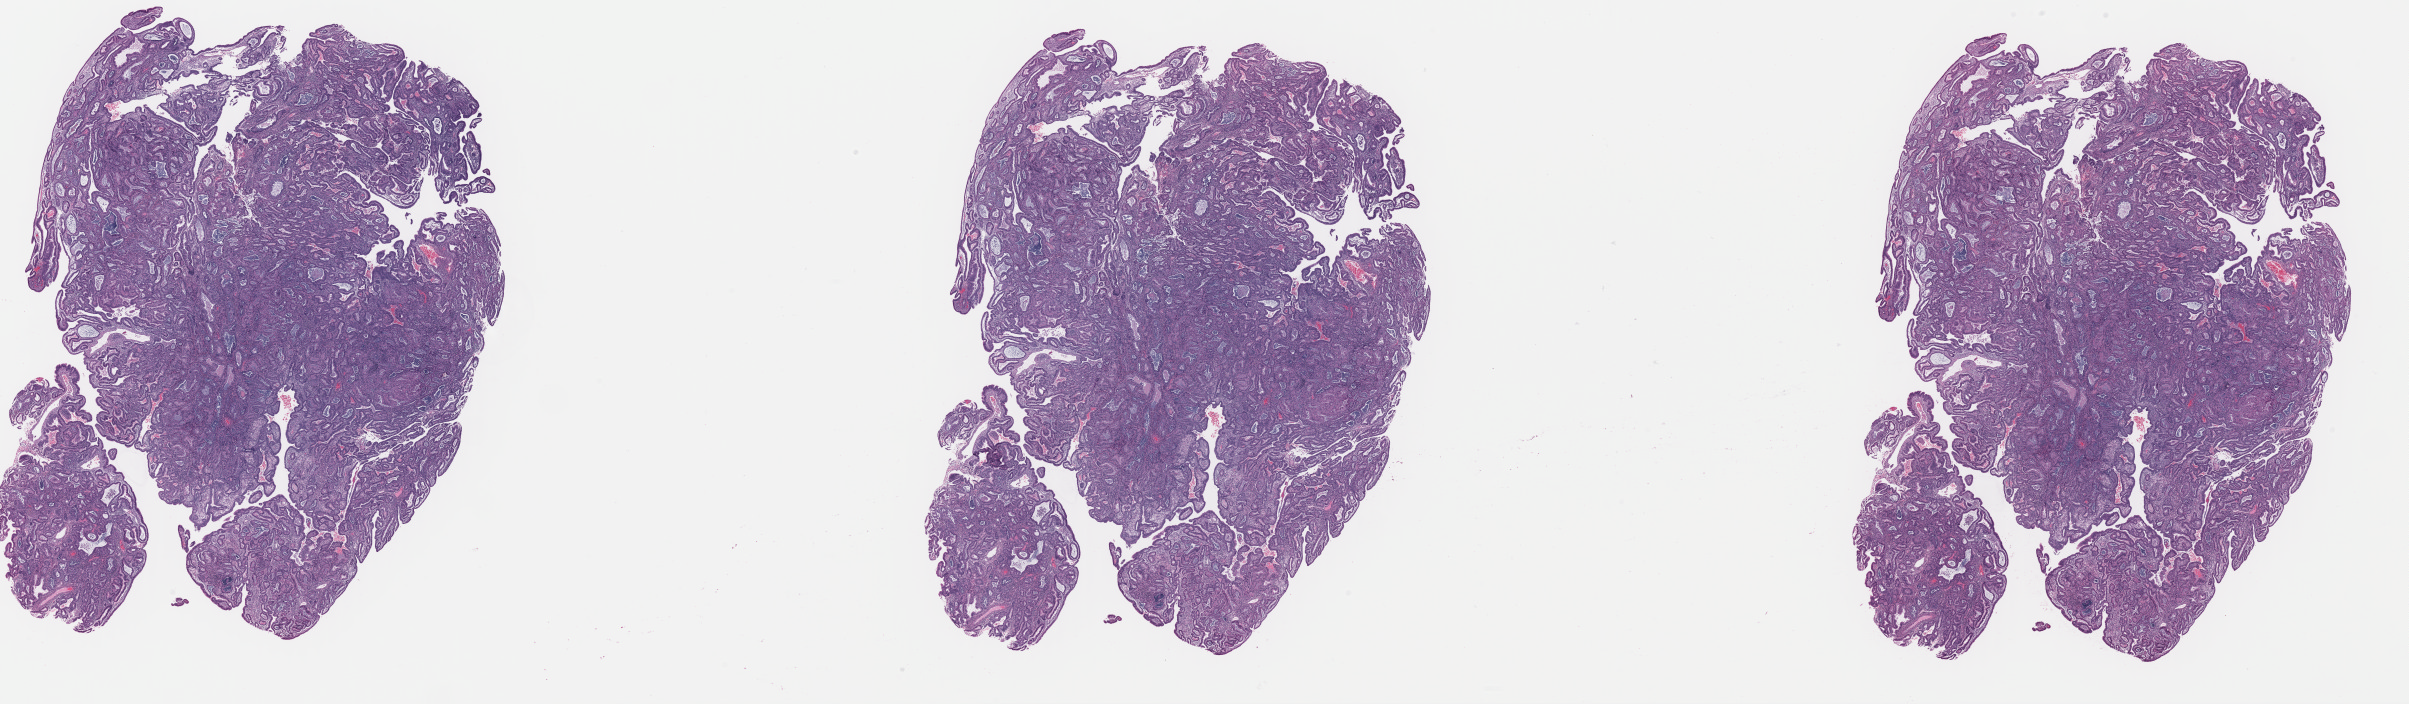
Hematoxylin and eosin (H&E) stained whole-slide image, shown as a low-resolution overview of the whole scanned area (about 38.1 x 11.1 mm); formalin-fixed paraffin-embedded (FFPE) diagnostic section; uterus, primary tumour sample. Female, age 67 years at initial diagnosis. Histologic grade: G1 (well differentiated).
FIGO stage: IA. Pathologic diagnosis: Endometrioid adenocarcinoma, NOS (endometrium). Lymph nodes positive (case pathology): 0 of 10 examined.